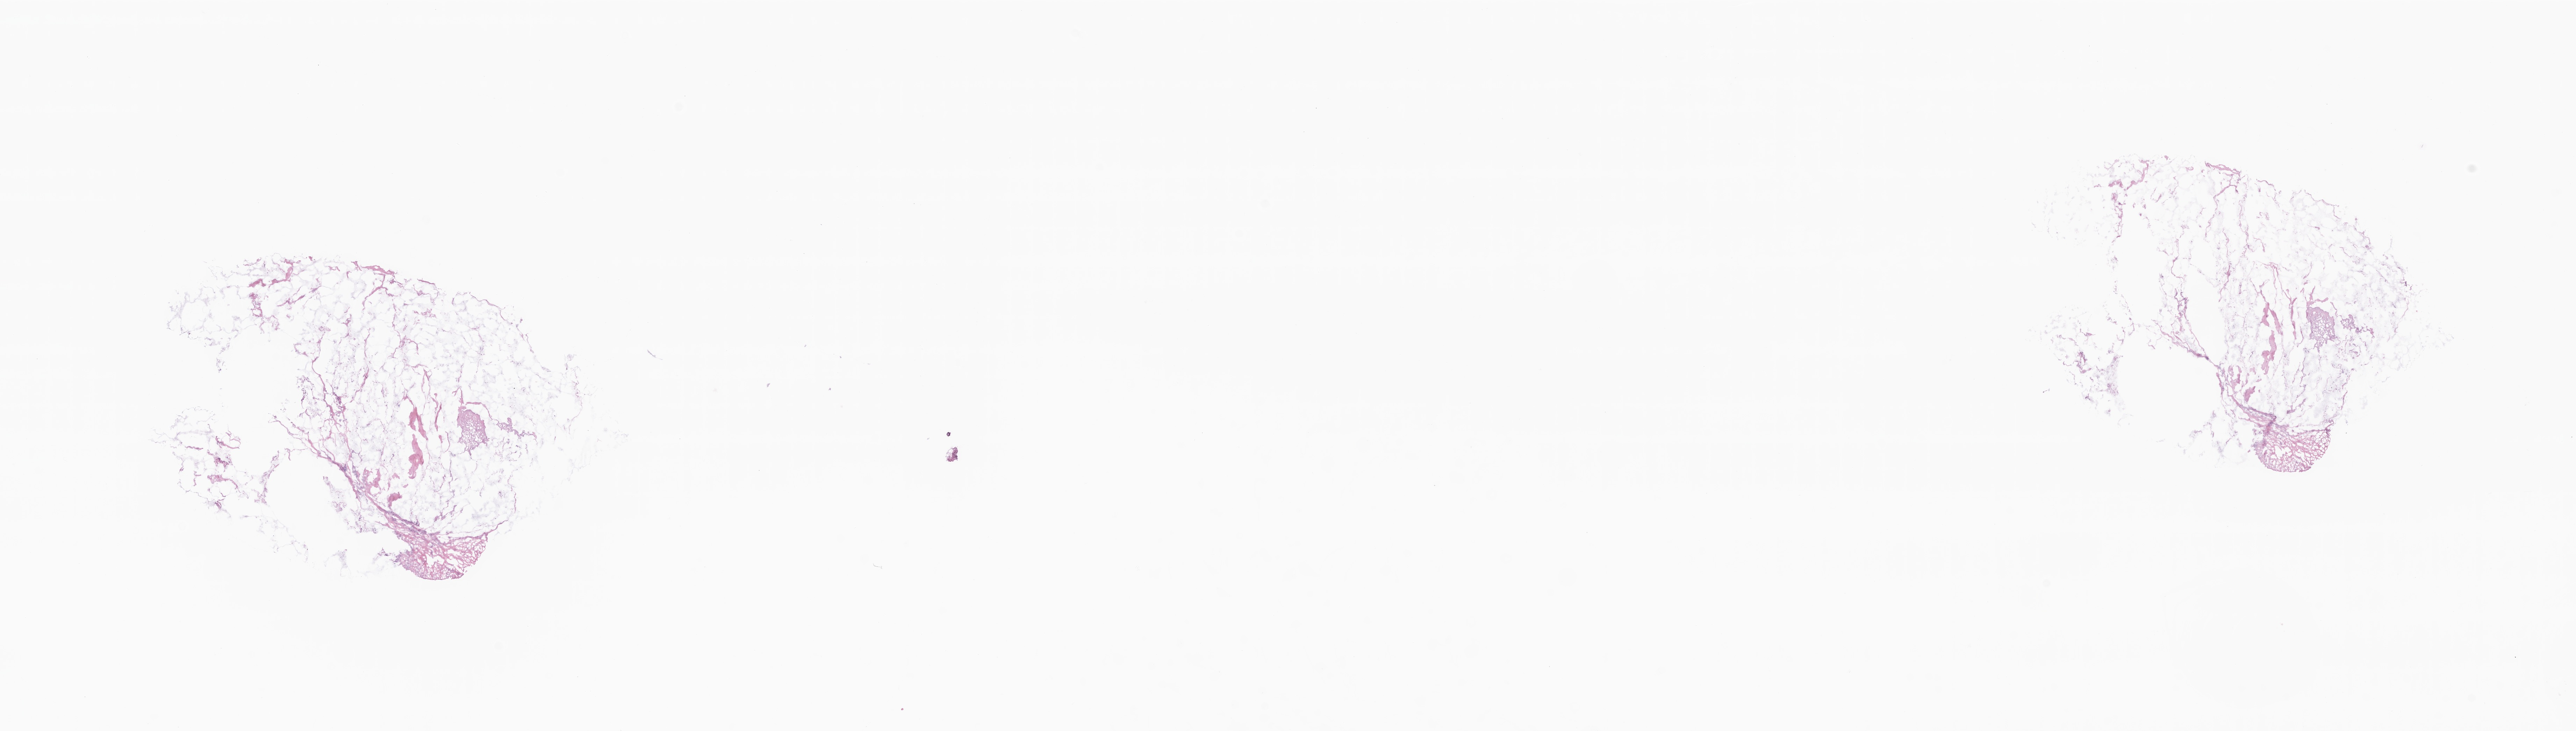
Whole-slide image, H&E stain — shown as a low-resolution overview of the whole scanned area (about 31.1 x 8.8 mm). Frozen section. Specimen: primary tumor. Site: breast (left). Female patient; age at initial diagnosis 73 years. Slide review estimates, as recorded: tumor cells 1%, tumor nuclei 20%, stromal cells 99%, necrosis 0%, normal cells 0%. Infiltration values recorded for this section: lymphocyte infiltration 2%, monocyte infiltration 0%, neutrophil infiltration 0%.
Diagnosis: Infiltrating duct carcinoma, NOS.